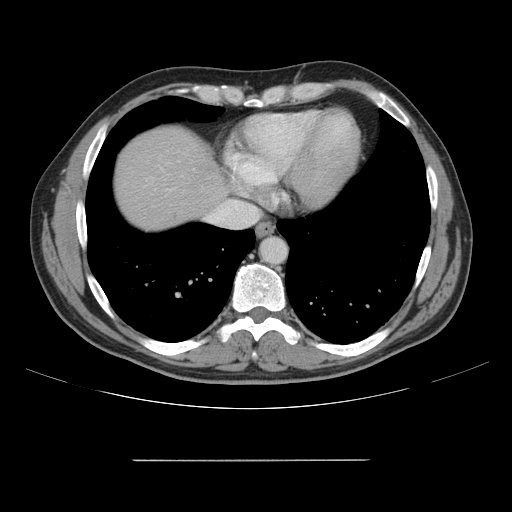
Contrast-enhanced abdominal CT, one axial slice. Slice 143 of 164 in the series (ordered by position). 120 kVp. Intravenous contrast given. Soft-tissue window (W 400 / L 40 HU). 2.5 mm slice thickness. 512 × 512 image matrix, field of view 404 × 404 mm. Male patient, age 54 years. From the clinical record (not read from this slice): diagnosis: colorectal cancer liver metastases, imaged before liver resection; multiple liver metastases: yes; largest metastasis: 1 cm; disease in both lobes: no.
Annotated regions visible in this slice (expert manual segmentation):
- hepatic veins: bounding box [x1, y1, x2, y2] px = [206, 200, 258, 228]
- liver: [114, 126, 224, 231]
- planned liver remnant (the part of the liver to remain after resection): [114, 126, 225, 231]